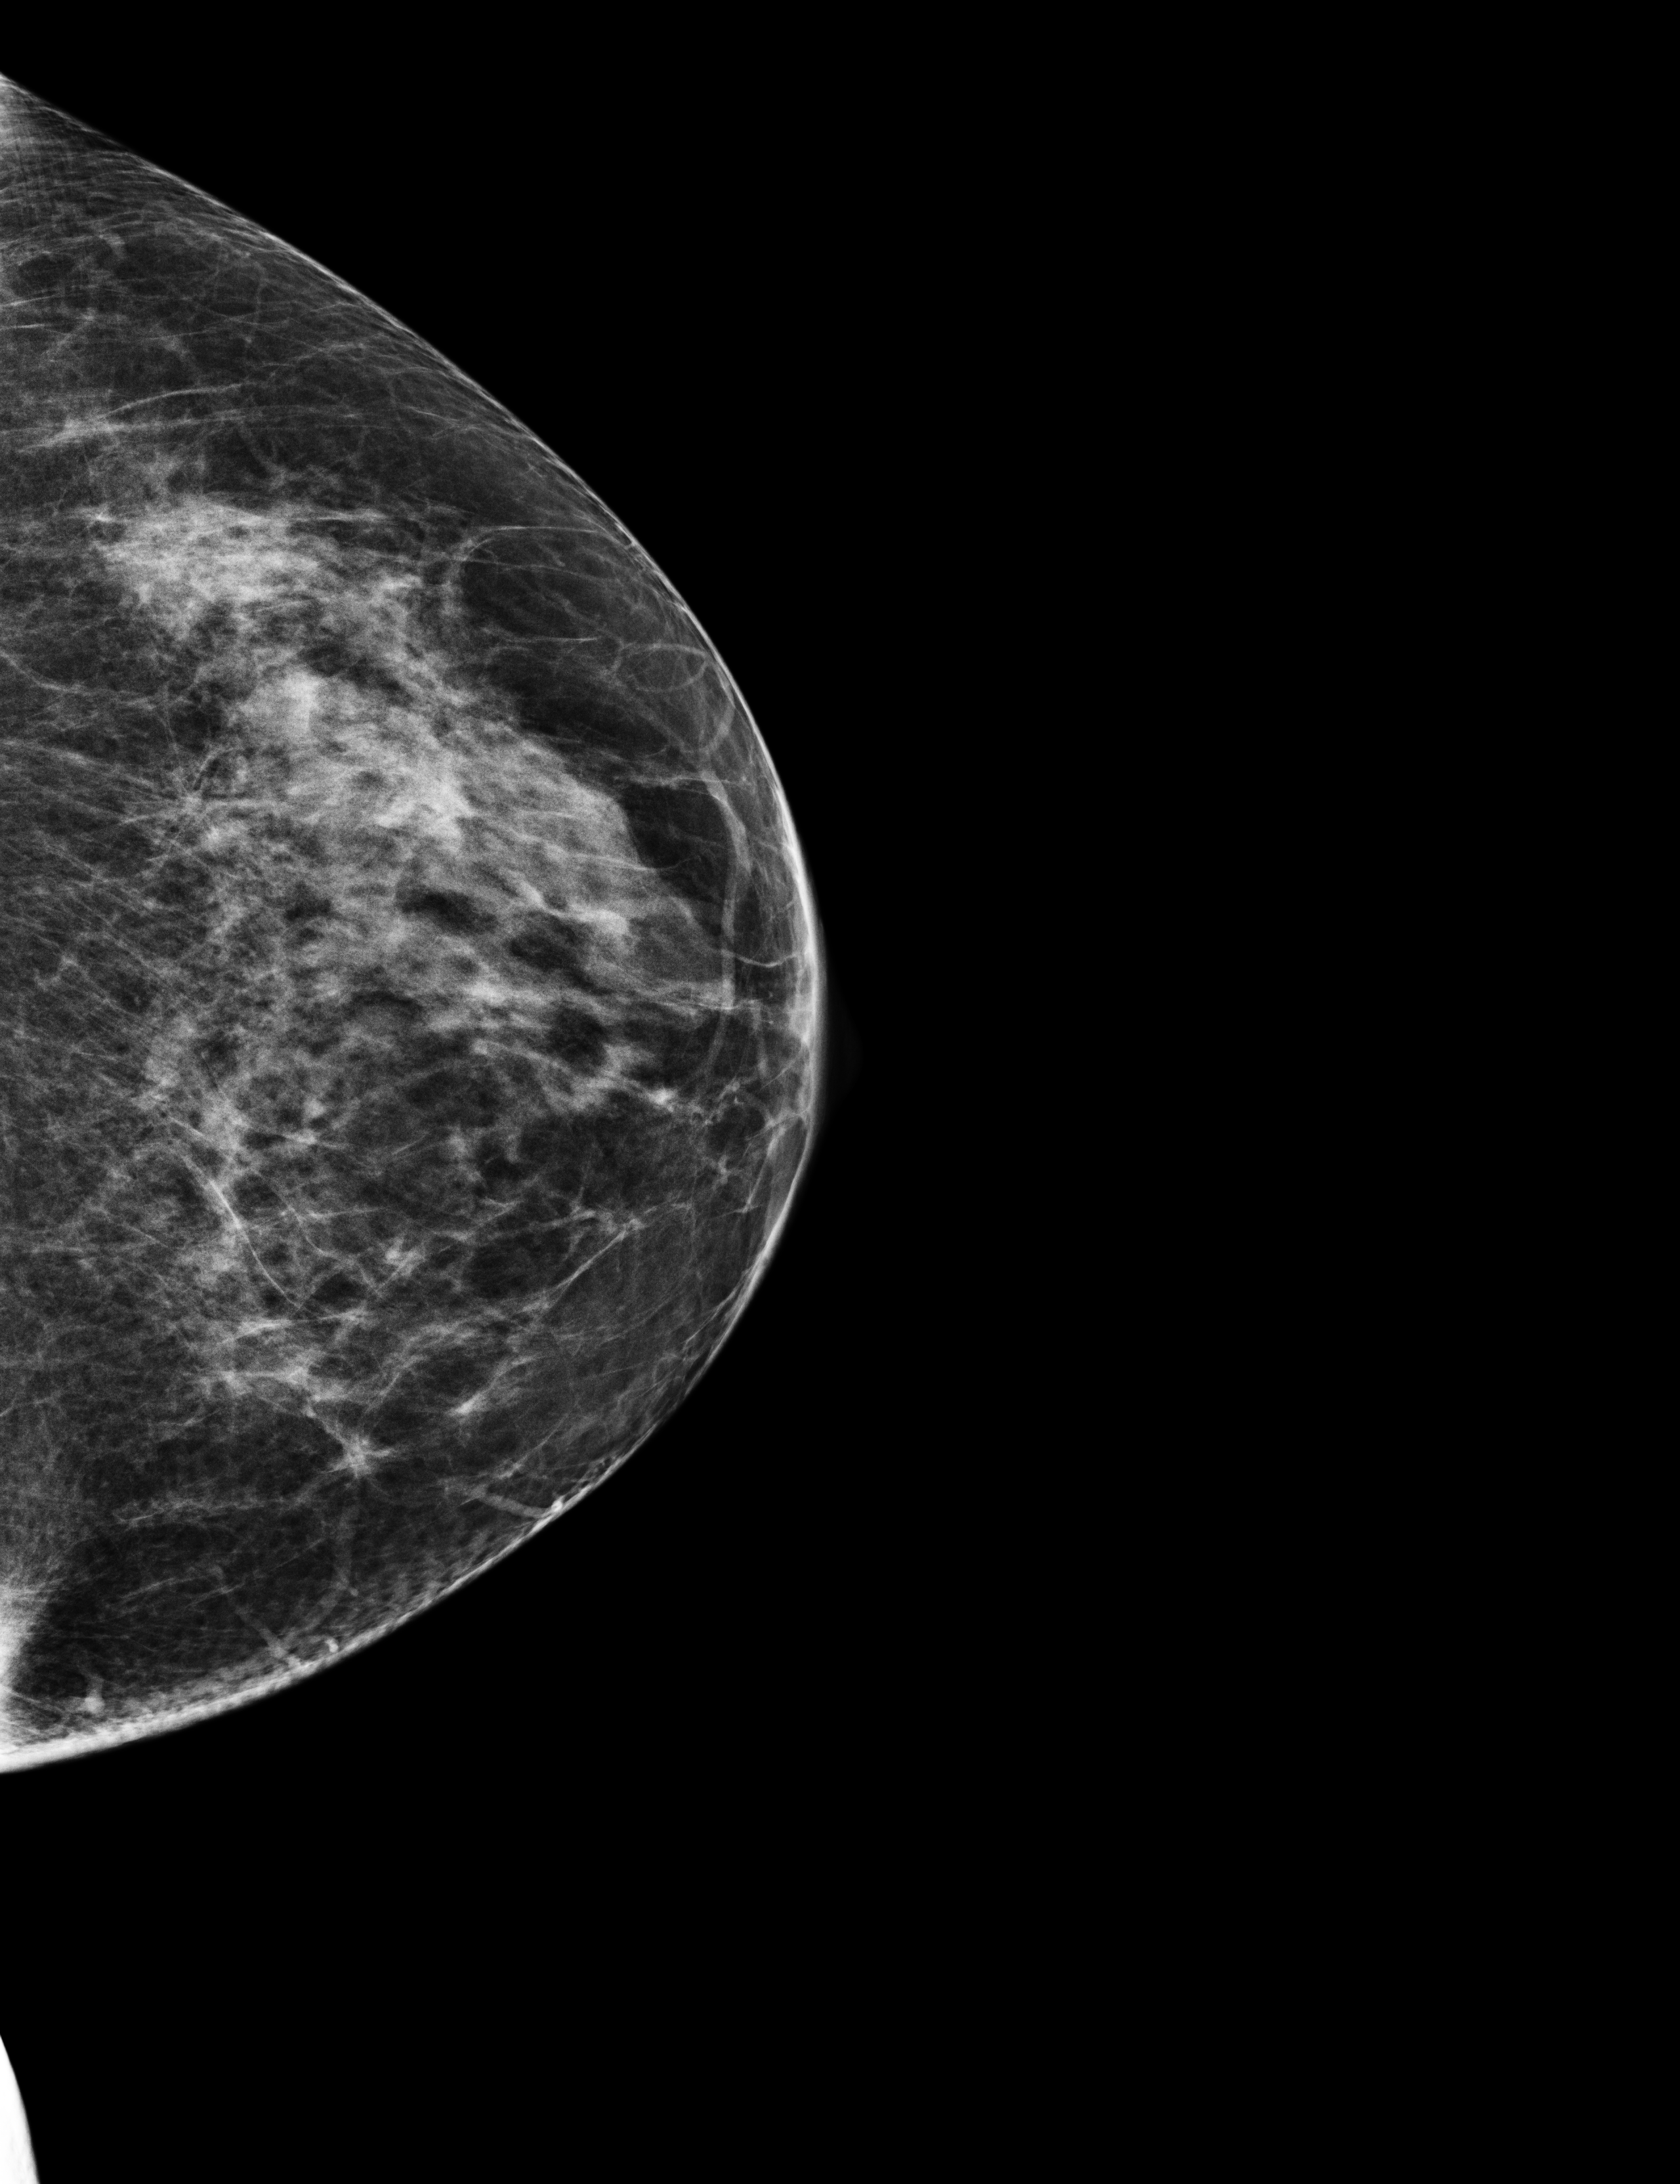
Full-field digital mammogram (FFDM); left breast; CC view; annual screening mammography examination. Female patient, age 56 years.
- breast density at the screening exam (both breasts): heterogeneously dense (BI-RADS density category c)
- final BI-RADS assessment for this screening round (tomosynthesis exam, both breasts): category 1
- recall: no recall after this screen